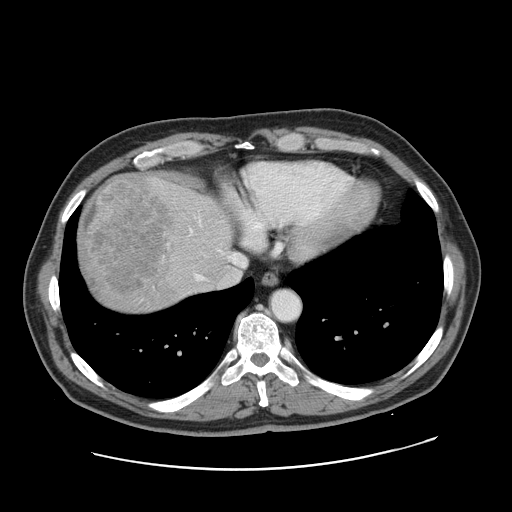
Contrast-enhanced abdominal CT, one axial slice; position 144 of 178 along the scan axis; 120 kVp; intravenous contrast given; soft-tissue window (W 400 / L 40 HU); 2.5 mm slice thickness; 512 × 512 image matrix. Male patient, age 63 years. Case-level facts recorded for this patient, not image findings: diagnosis: colorectal cancer liver metastases, imaged before liver resection; multiple liver metastases: yes.
Structures marked on this image (expert manual segmentation):
- hepatic veins: bounding box [x1, y1, x2, y2] px = [196, 249, 246, 280]
- liver: [78, 173, 233, 313]
- planned liver remnant (the part of the liver to remain after resection): [183, 188, 232, 264]
- liver metastasis: [81, 176, 173, 295]